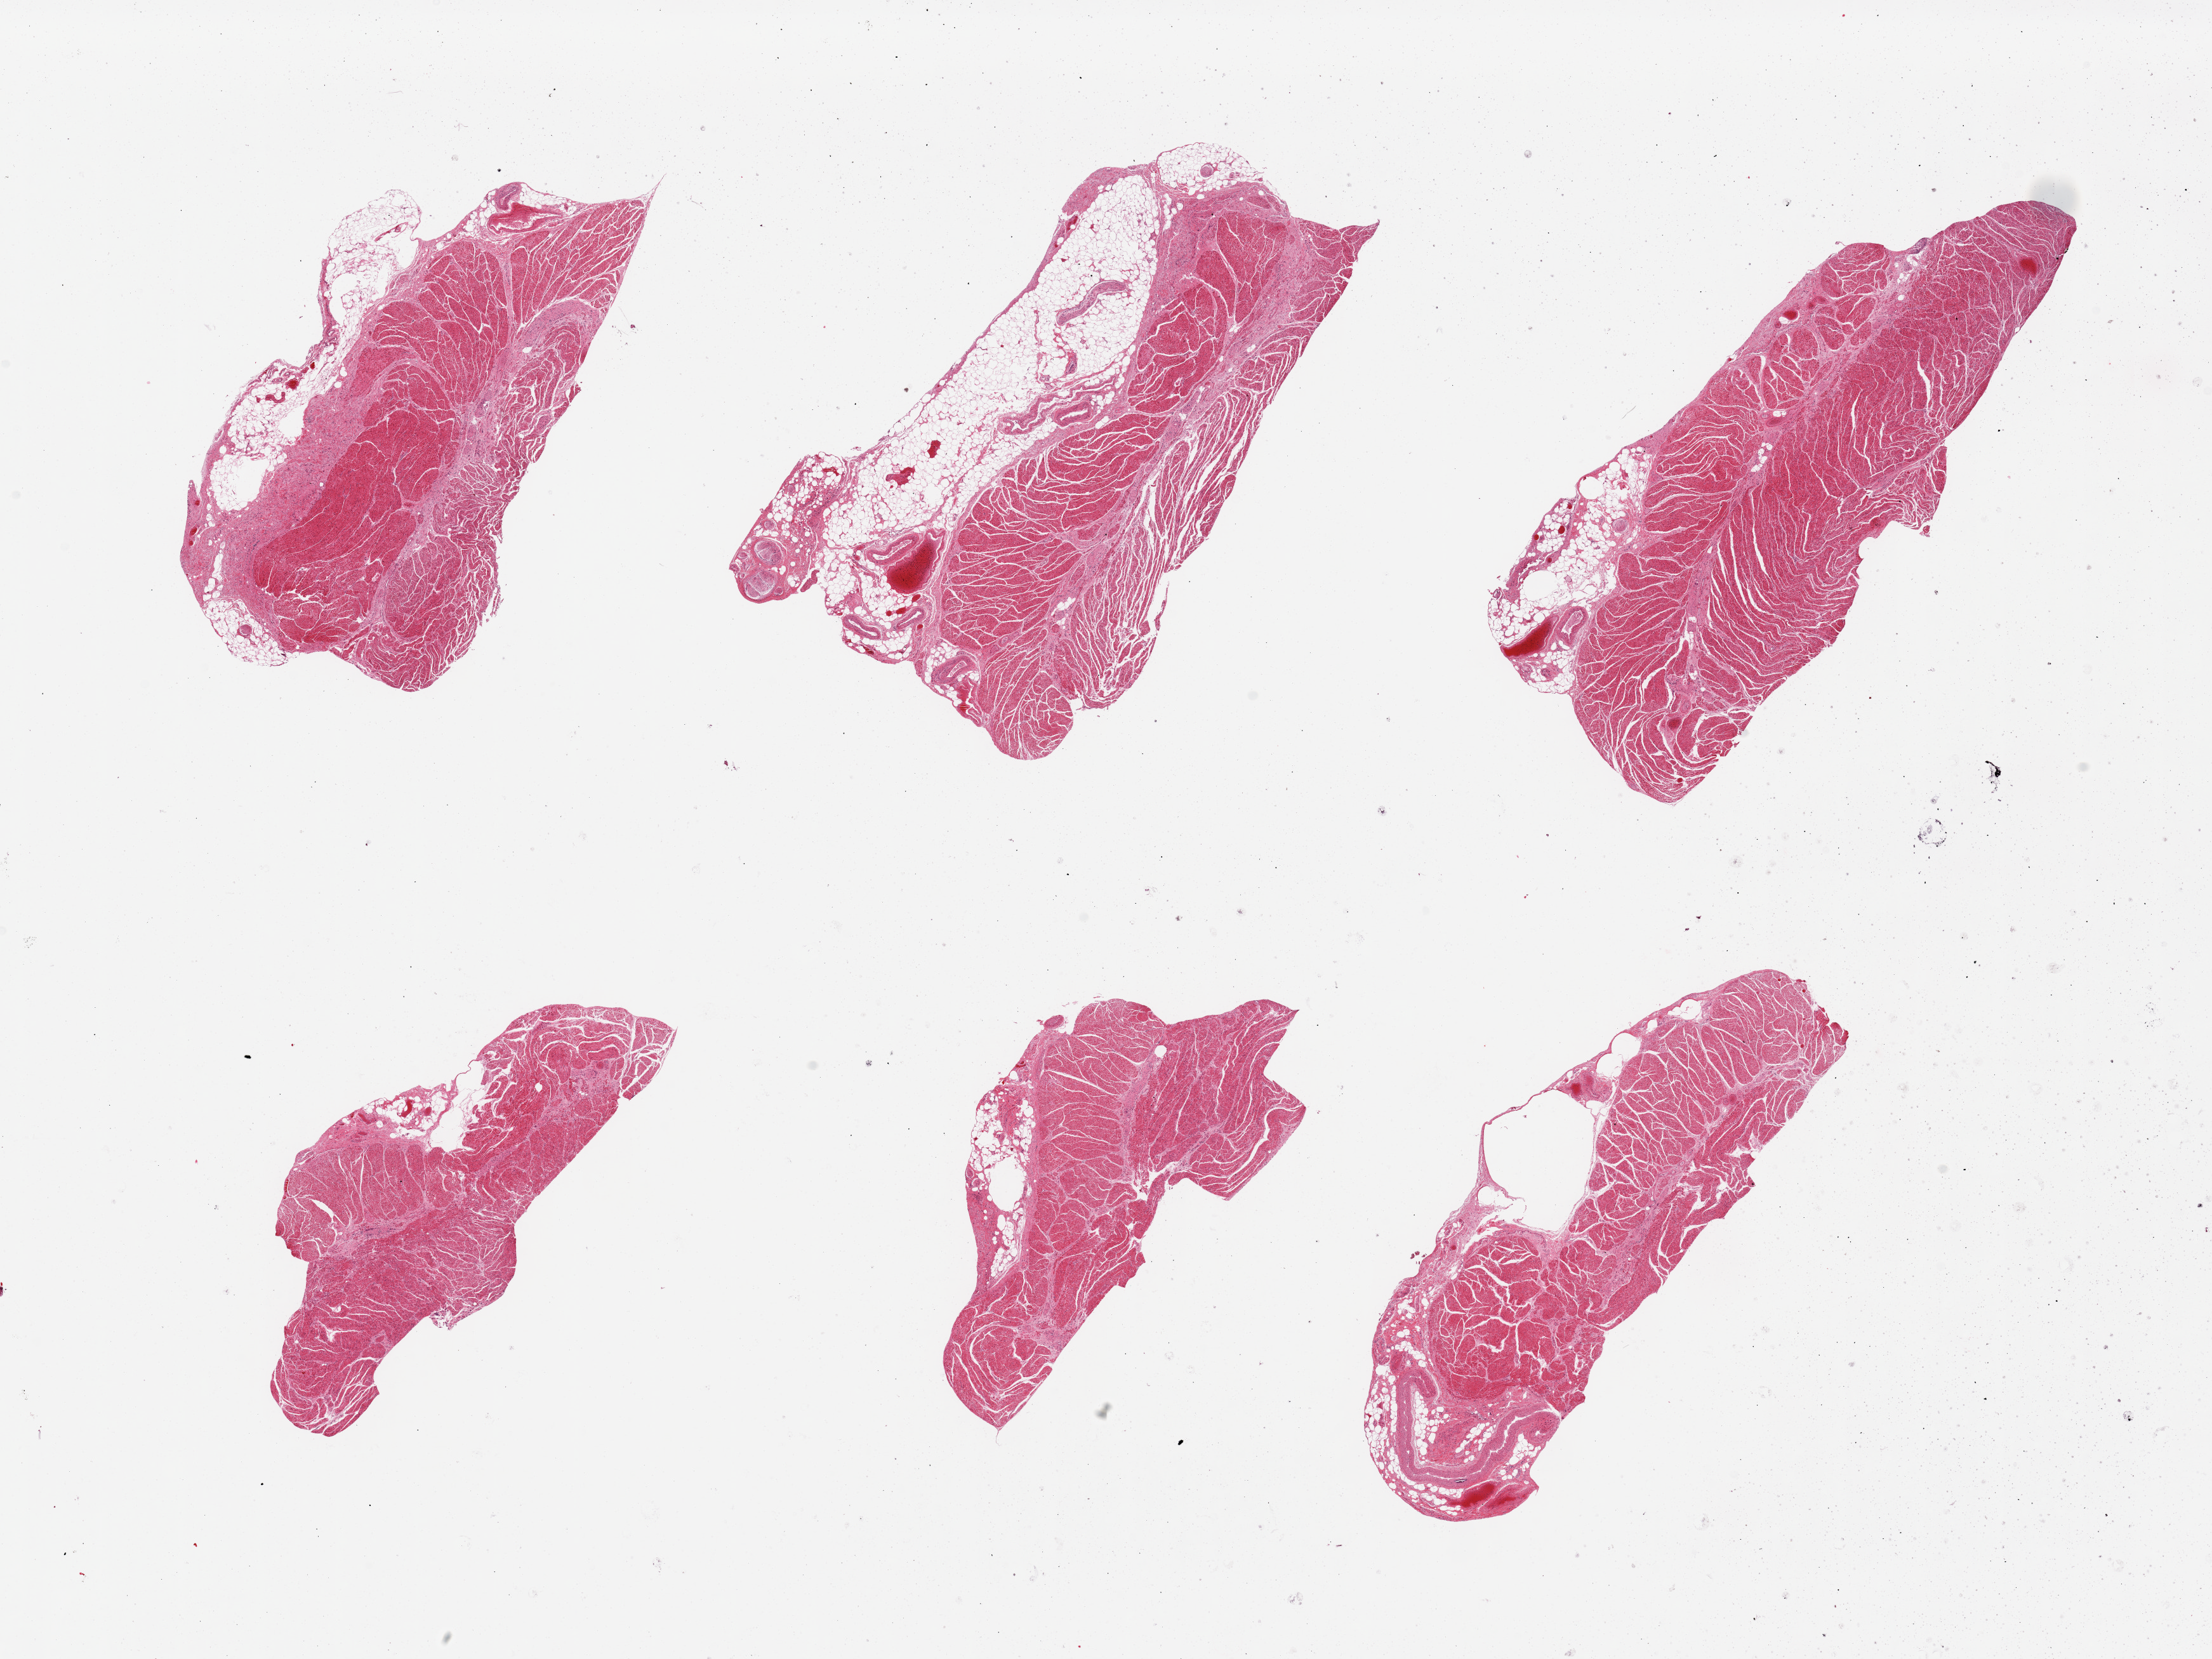
H&E whole-slide image — low-resolution overview of the scanned area, about 27.6 x 20.7 mm; PAXgene-fixed, paraffin-embedded tissue; sampled site (target tissue): gastroesophageal junction; tissue donor sample.
• review note (as recorded): 6 pieces, some with attached adipose tissue